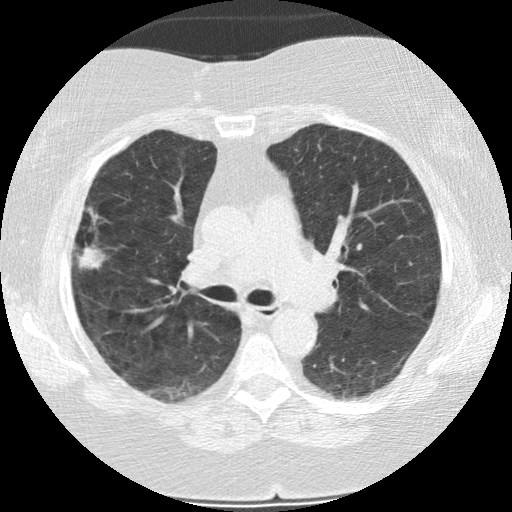
Low-dose screening chest CT, axial slice, baseline annual screen, lung window (W 1500 / L -600 HU), standard (soft-tissue) reconstruction kernel (STANDARD), 120 kVp, 512 × 512 image matrix, field of view 320 × 320 mm. Female, age 73 years at enrolment. Former smoker at enrolment.
- Expert reader's lesion annotation, bounding box <59,212,112,277> (left, top, right, bottom; pixels).
- Reader record for this screening exam (exam-level; its link to the box is not recorded): non-calcified nodule or mass ≥4 mm, right upper lobe, 21 × 14 mm, poorly defined margins, soft tissue attenuation.
- Later outcome: lung cancer diagnosed 482 days after this screen (after the second annual screen) — bronchiolo-alveolar adenocarcinoma, NOS, right upper lobe, moderately differentiated (G2), stage IIIB (AJCC 6th edition), 21 mm at pathology.